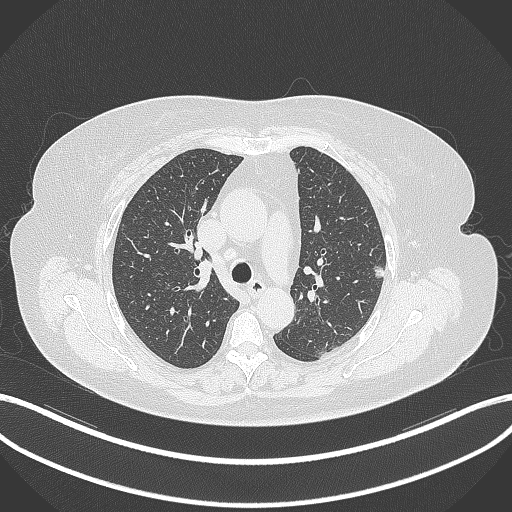
Chest CT, one axial slice; position 218 of 309 along the scan axis; reconstruction kernel B70f; 120 kVp; lung window (W 1500 / L -600 HU); 1 mm slice thickness; 512 × 512 image matrix, field of view 400 × 400 mm. Patient: female, 70 years. Case-level facts recorded for this patient, not image findings: clinical TNM (as recorded): T1c N0 M0.
Annotated regions visible in this slice (rectangle marked by the reading radiologist):
- lung tumour (recorded histology: adenocarcinoma): bounding box <370,261,385,282> (left, top, right, bottom; pixels)